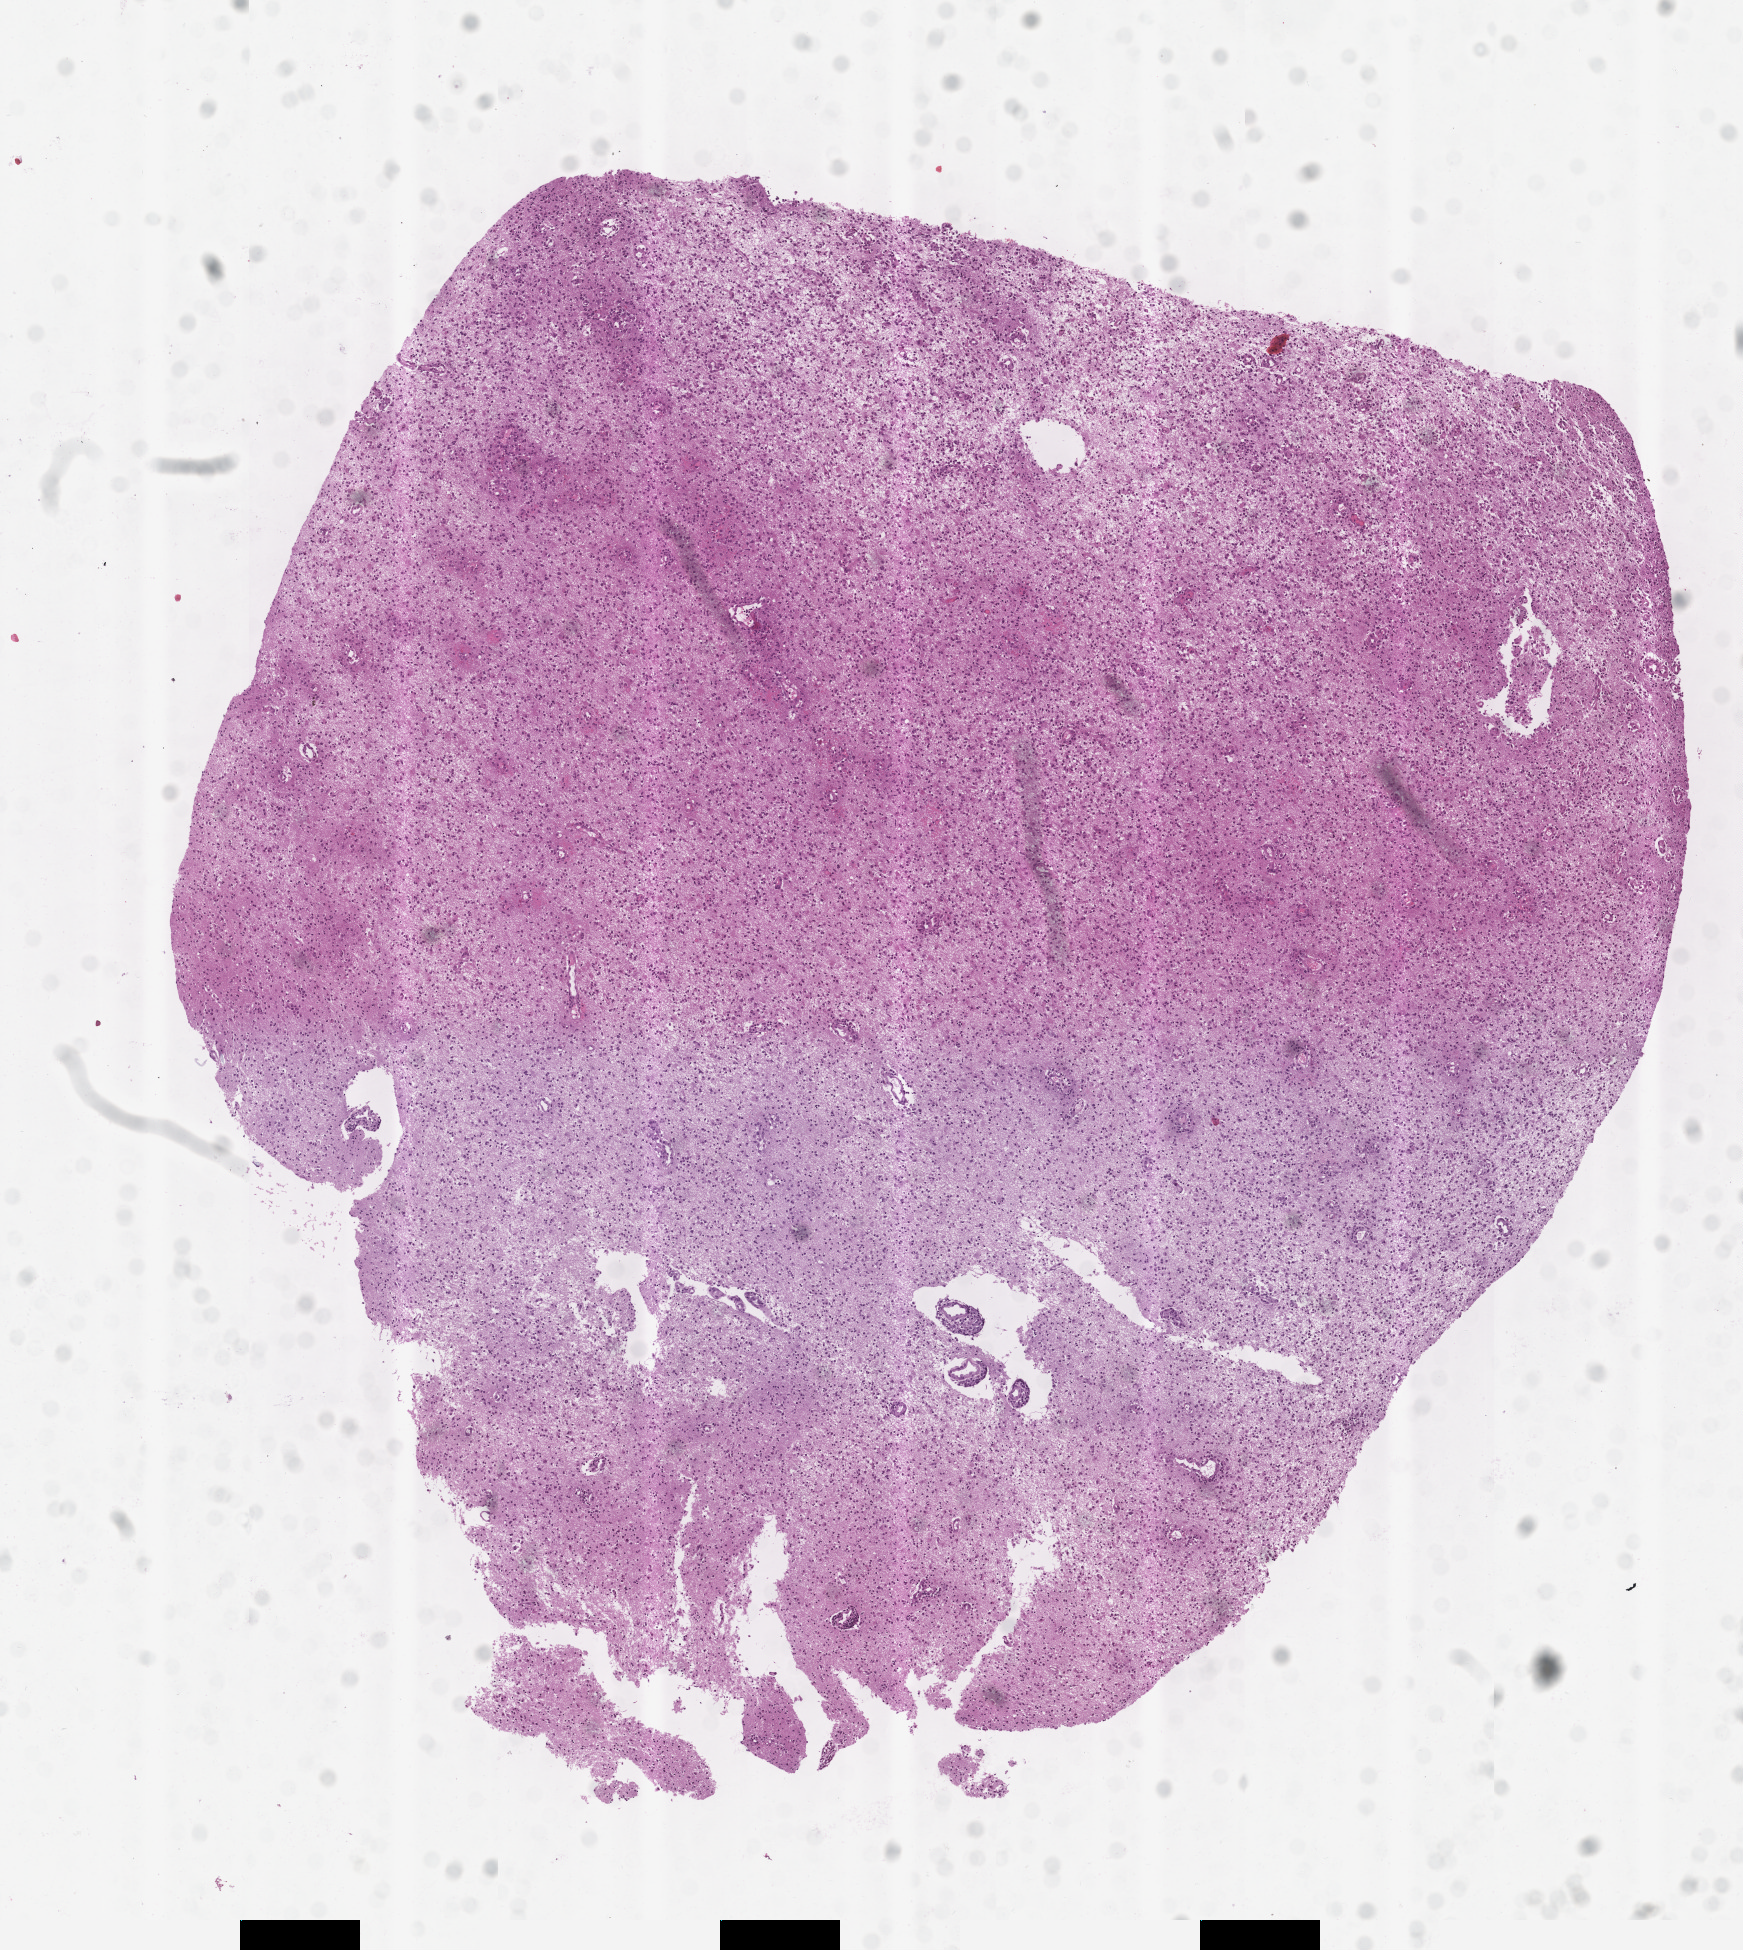
H&E-stained whole-slide image, whole scanned area (about 7.0 x 7.9 mm, slide scanned at 20x) shown as a low-resolution overview; tumour tissue sample, sampled site: frontal lobe. Male, 39 y/o. Pathologist review of this section (percent, as recorded): tumour nuclei 70%, necrosis 7%.
• primary tumour site (as recorded): frontal lobe
• histologic diagnosis: Glioblastoma